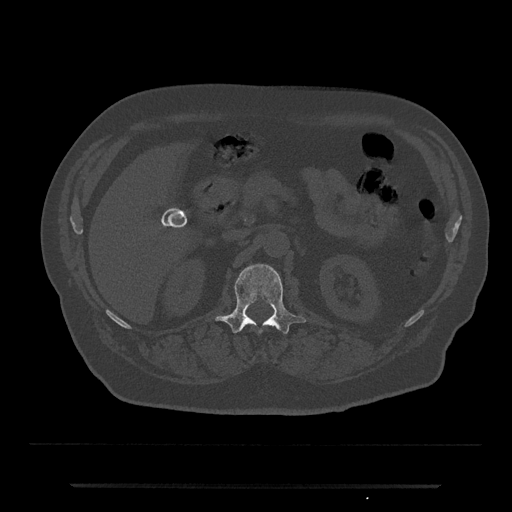
CT including the spine, one axial slice; bone window (W 1800 / L 400 HU); 512 × 512 image matrix, field of view 434 × 434 mm. Male patient, age 80 years. From the clinical record (not read from this slice): primary cancer: prostate.
Annotated regions visible in this slice (semi-automatic segmentation, software-assisted and operator-edited):
- L1 vertebra: bounding box [x1, y1, x2, y2] px = [215, 264, 306, 334]